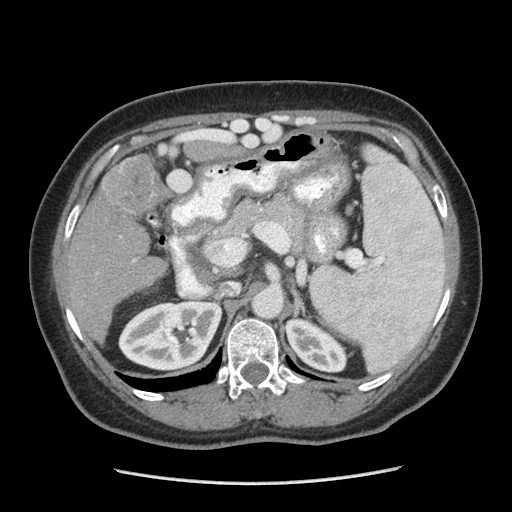
Contrast-enhanced abdominal CT (liver protocol), one axial slice; slice 146 of 185 in the series (ordered by position); 140 kVp; soft-tissue window (W 400 / L 40 HU); 2.5 mm slice thickness; 512 × 512 image matrix, field of view 360 × 360 mm. Case-level facts recorded for this patient, not image findings: diagnosis: hepatocellular carcinoma (patient treated with transarterial chemoembolisation; whether this scan precedes or follows treatment is not stated here); TNM stage (as recorded): Stage-I; Child-Pugh class: A; tumour differentiation: poorly differentiated; tumour nodularity: uninodular.
Structures marked on this image (semi-automatically segmented with operator editing):
- liver parenchyma outside the tumour (the mass and vessels are separate outlines, so this box may not span the whole liver): bounding box (x1, y1, x2, y2) in pixels: (62, 154, 166, 340)
- mass: (99, 156, 166, 216)